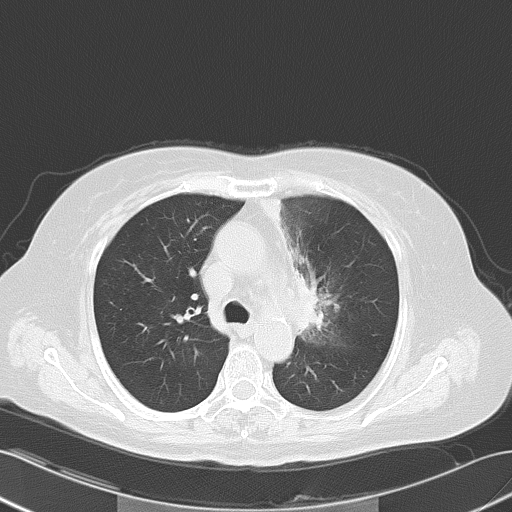
Chest CT, one axial slice; slice 38 of 56 in the series (ordered by position); reconstruction kernel B70f; lung window (W 1500 / L -600 HU); 5 mm slice thickness; 512 × 512 image matrix. Patient: female, 65 years. Case-level facts recorded for this patient, not image findings: clinical TNM (as recorded): T2b N1 M0.
Annotated regions visible in this slice (rectangle marked by the reading radiologist):
- lung tumour (recorded histology: adenocarcinoma): bounding box (x1, y1, x2, y2) in pixels: (296, 266, 334, 342)